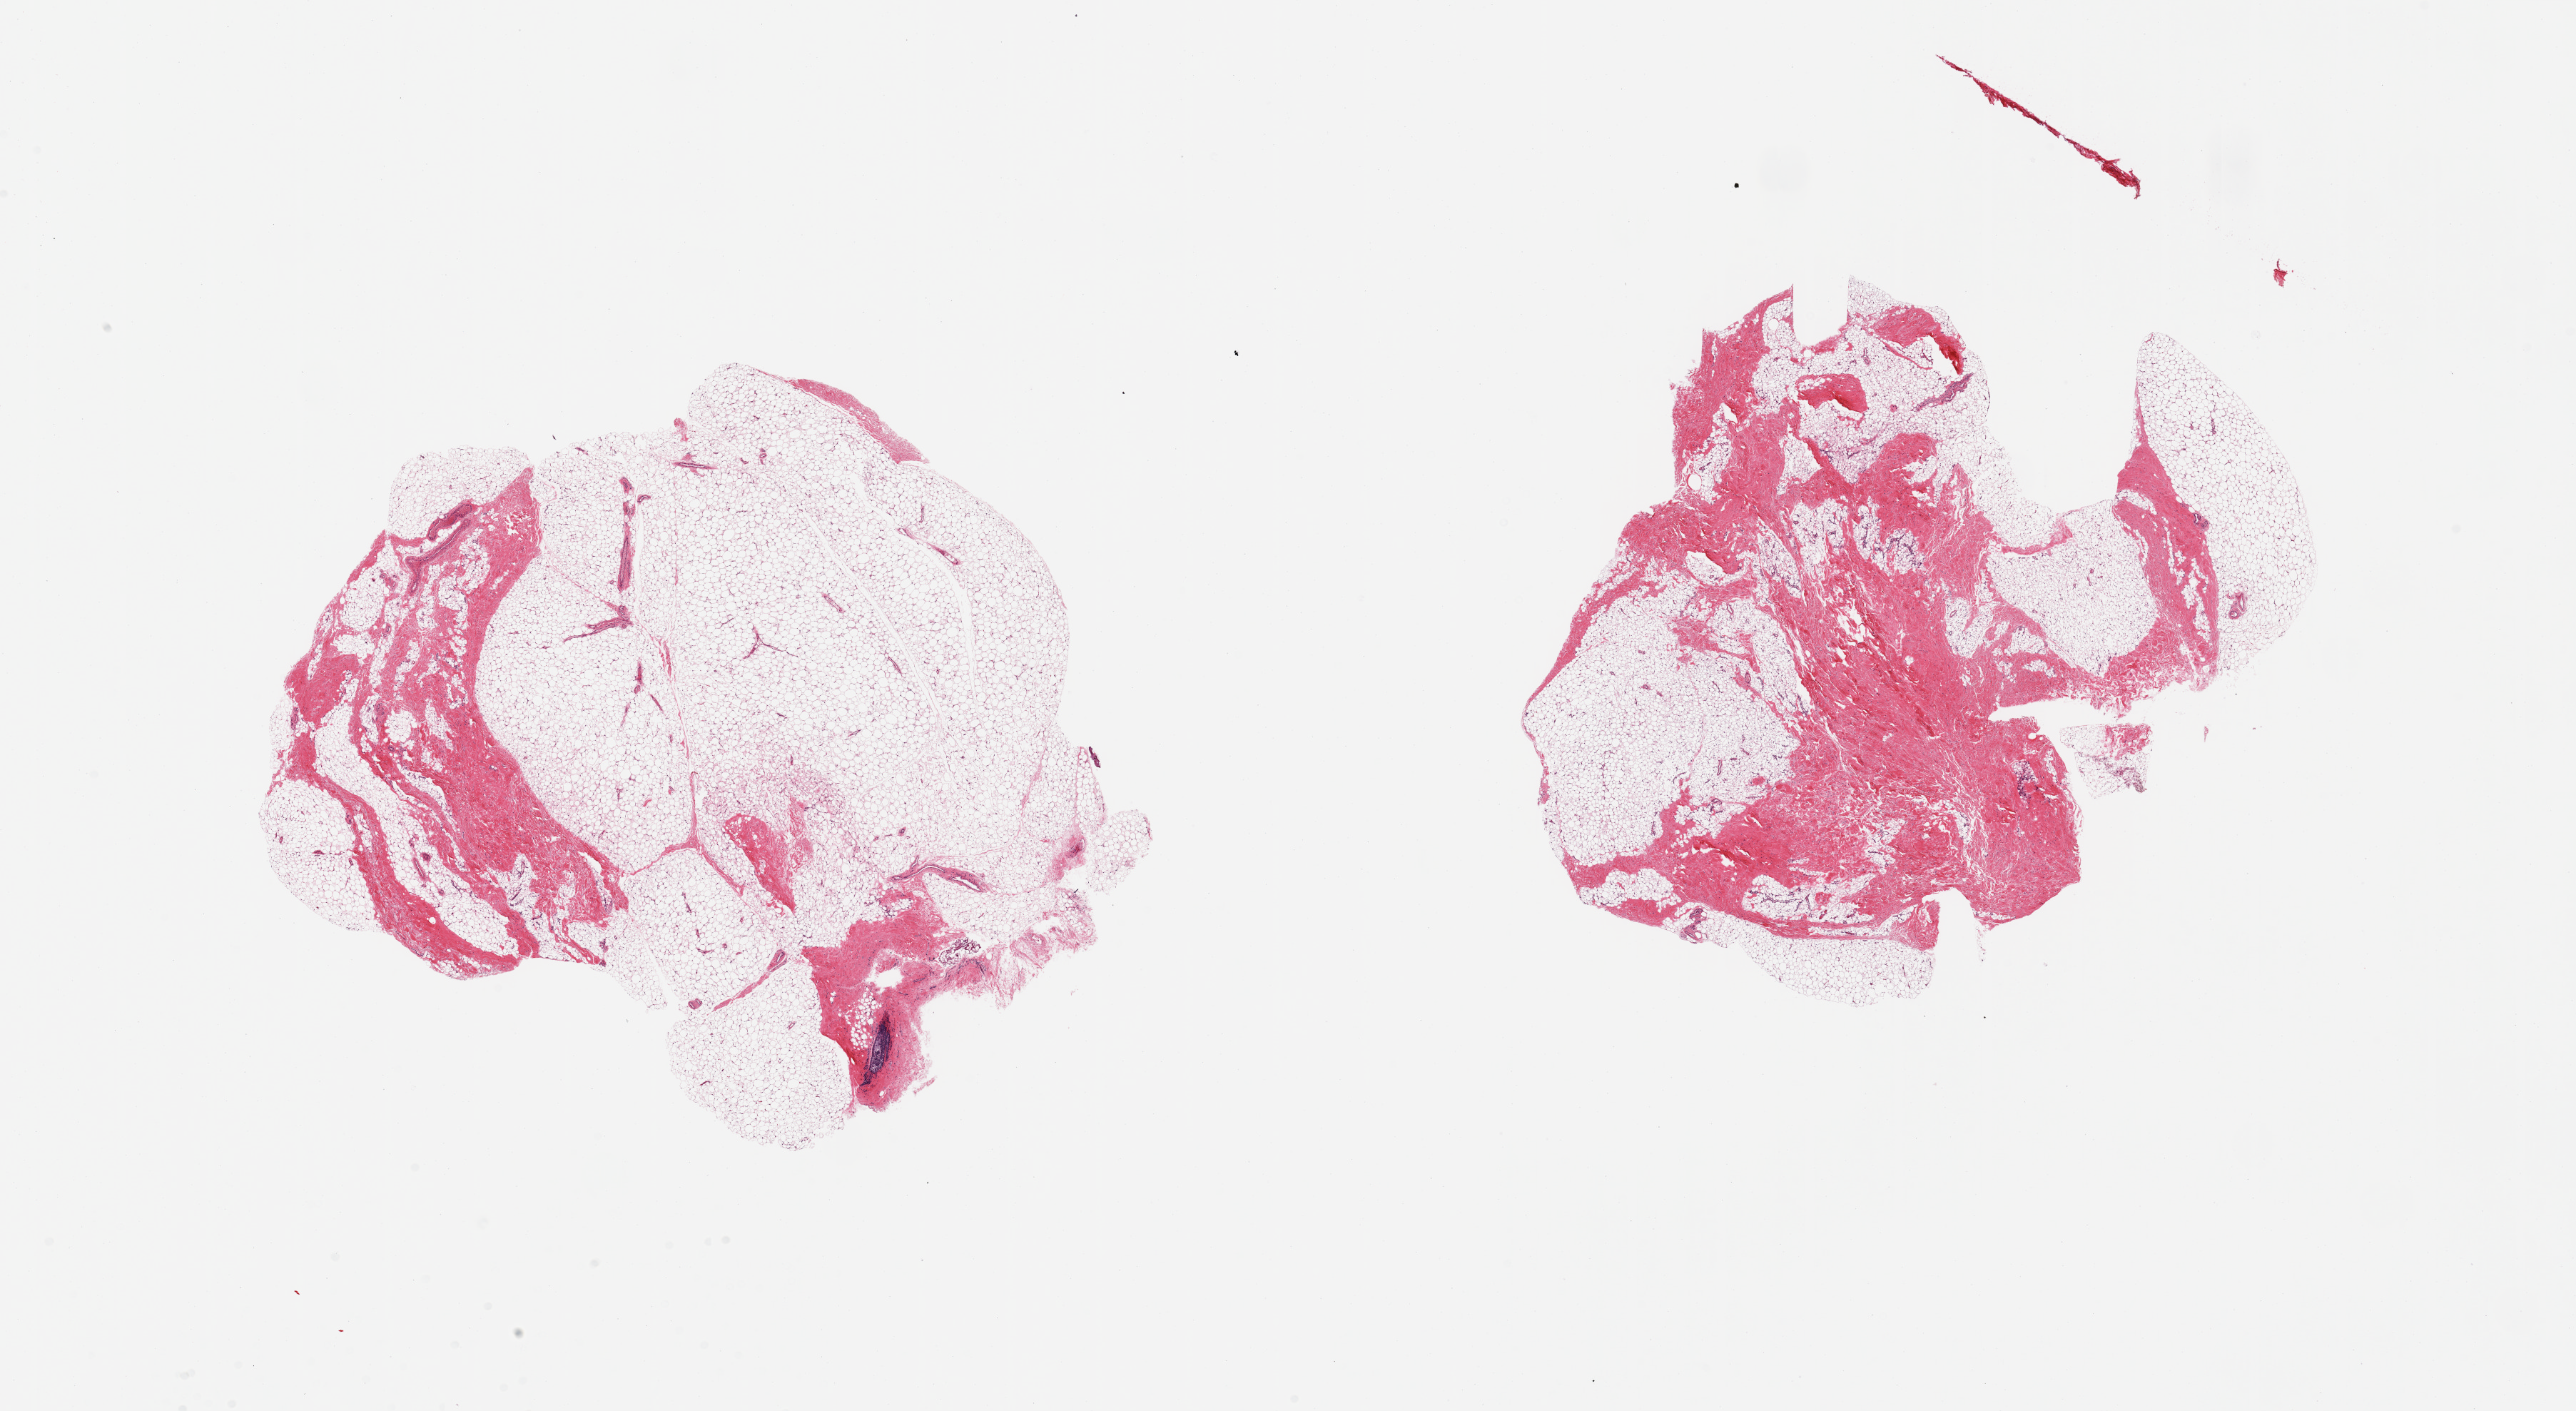
Whole-slide image, hematoxylin and eosin (H&E) stain, shown as a low-resolution overview of the whole scanned area (about 28.5 x 15.6 mm); PAXgene-fixed, paraffin-embedded tissue; section of breast (target tissue); donor tissue sample. Donor: male.
Review note (as recorded): 2 pieces; fibroadipose tissue; 1 has mammary duct.